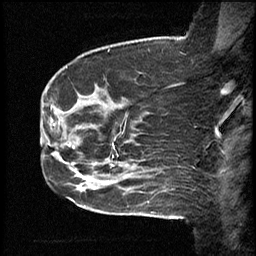
Breast MRI (dynamic contrast-enhanced), one sagittal slice. Slice 15 of 46 in the series (ordered by position). Dynamic contrast-enhanced study with each time point stored as its own series, time point 2 of 4 at this slice position (early post-contrast, ordered by acquisition time). 1.5 T. TE 4.2 ms, TR 18.3 ms. 3 mm slice thickness. 256 × 256 image matrix. Case-level facts recorded for this patient, not image findings: setting: breast cancer imaged before/during neoadjuvant chemotherapy; receptor status: HR-positive, HER2-negative.
Outlined on this slice (semi-automatic segmentation, software-assisted and operator-edited):
- analysis volume of interest (the breast-tissue region the enhancement analysis was run in; not a lesion): bounding box <64,84,111,209> (left, top, right, bottom; pixels)
- tumour enhancement mask (voxels above the 100 % enhancement threshold inside the analysis volume of interest): <88,178,90,180>